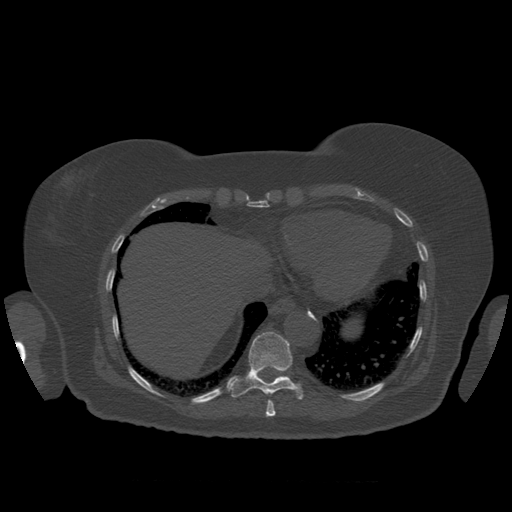
CT including the spine, one axial slice. Slice 342 of 399 in the series (ordered by position). Reconstruction kernel STANDARD. Bone window (W 1800 / L 400 HU). 1.25 mm slice thickness. 512 × 512 image matrix, field of view 404 × 404 mm. Patient age 81 years. From the clinical record (not read from this slice): primary cancer: renal.
Structures marked on this image (semi-automatically segmented with operator editing):
- T10 vertebra: bounding box <232,332,304,400> (left, top, right, bottom; pixels)
- T9 vertebra: <266,400,276,417>